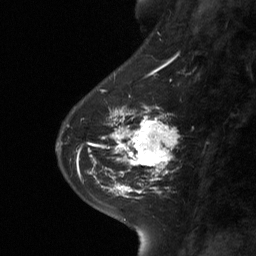
Breast MRI (dynamic contrast-enhanced), one sagittal slice. Dynamic contrast-enhanced study with each time point stored as its own series, time point 2 of 3 at this slice position (early post-contrast, ordered by acquisition time). 1.5 T. TE 4.8 ms, TR 27 ms. 2 mm slice thickness. 256 × 256 image matrix, field of view 180 × 180 mm. Patient: female, 42 years. Case-level facts recorded for this patient, not image findings: setting: breast cancer imaged before/during neoadjuvant chemotherapy; receptor status: triple-negative.
Outlined on this slice (semi-automatic segmentation, software-assisted and operator-edited):
- analysis volume of interest (the breast-tissue region the enhancement analysis was run in; not a lesion): box from (x=111, y=104) to (x=178, y=178) px
- tumour enhancement mask (voxels above the 90 % enhancement threshold inside the analysis volume of interest): (x=111, y=106)–(x=175, y=178)